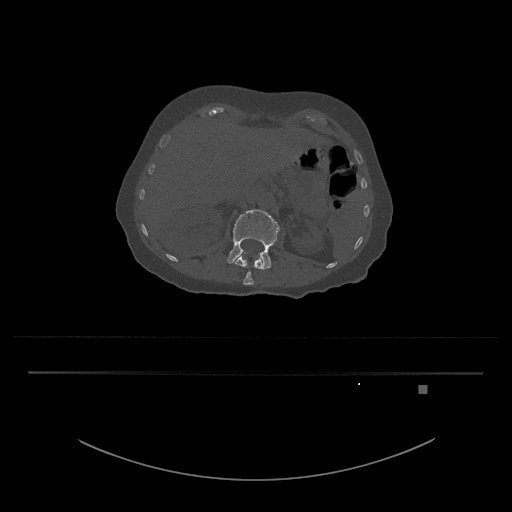
CT including the spine, one axial slice; slice 517 of 797 in the series (ordered by position); bone window (W 1800 / L 400 HU); 0.5 mm slice thickness; 512 × 512 image matrix, field of view 500 × 500 mm. Female patient, age 57 years. Case-level facts recorded for this patient, not image findings: primary cancer: cervical.
Structures marked on this image (semi-automatic segmentation, software-assisted and operator-edited):
- L1 vertebra: bounding box (x1, y1, x2, y2) in pixels: (235, 255, 263, 285)